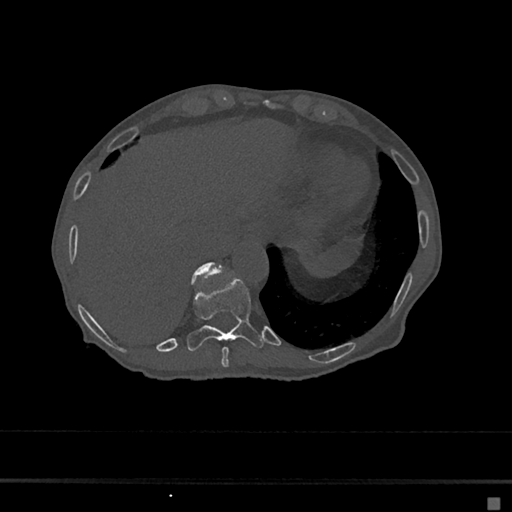
CT including the spine, one axial slice. Slice 227 of 797 in the series (ordered by position). Bone window (W 1800 / L 400 HU). 0.5 mm slice thickness. 512 × 512 image matrix. Patient: female, 68 years. From the clinical record (not read from this slice): primary cancer: renal.
Outlined on this slice (semi-automatic segmentation, software-assisted and operator-edited):
- T10 vertebra: box from (x=187, y=278) to (x=263, y=351) px
- T11 vertebra: (x=192, y=262)–(x=224, y=279)
- T9 vertebra: (x=221, y=347)–(x=229, y=367)